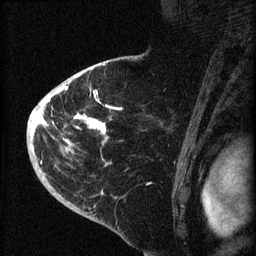
Breast MRI (dynamic contrast-enhanced), one sagittal slice. Position 48 of 60 along the scan axis. Dynamic contrast-enhanced series, image 2 of 4 at this slice position (ordered by acquisition). 1.5 T. TE 4.2 ms, TR 8.2 ms. 2 mm slice thickness. 256 × 256 image matrix, field of view 180 × 180 mm. Female patient, age 71 years.
Annotated regions visible in this slice (semi-automatic segmentation, software-assisted and operator-edited):
- analysis volume of interest (the breast-tissue region the enhancement analysis was run in; not a lesion): bounding box [x1, y1, x2, y2] px = [35, 75, 129, 190]
- tumour enhancement mask (voxels above the 70 % enhancement threshold inside the analysis volume of interest): [35, 85, 106, 164]